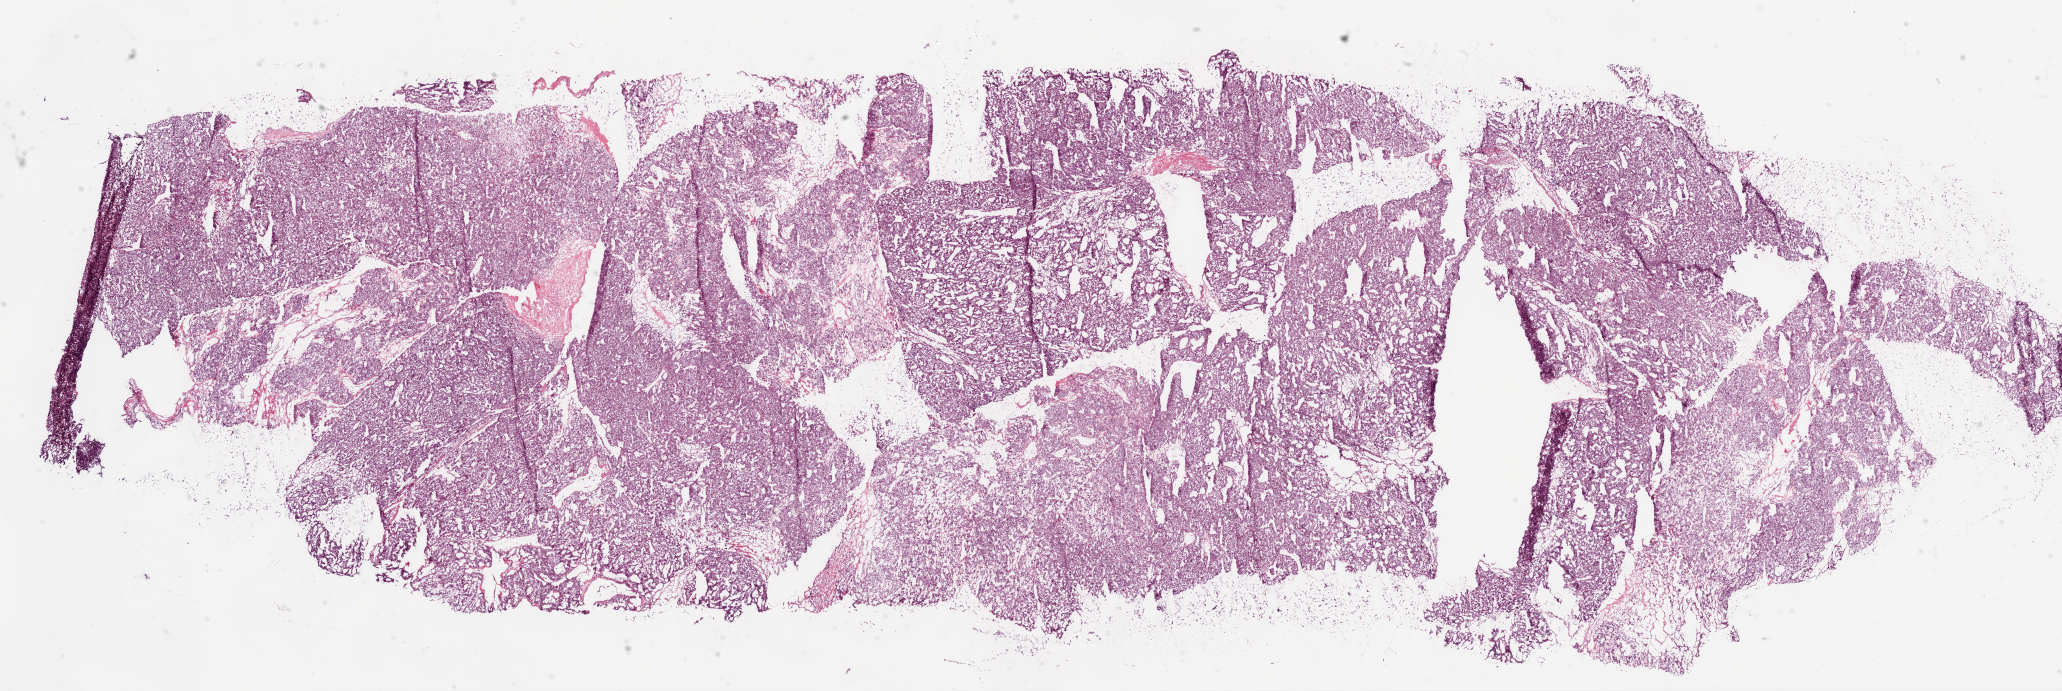
Whole-slide histology image, Hematoxylin and eosin (H&E) stained, low-resolution overview of the scanned area, about 33.1 x 11.1 mm (slide scanned at 20x). Frozen section from the bottom of the tissue portion. Primary tumour sample from the kidney. Male patient; age at initial diagnosis 57 years. Histologic grade: G3 (poorly differentiated). Slide review estimates, as recorded: tumour cells 90%, tumour nuclei 85%, normal cells 0%, stromal cells 10%, necrosis 0%.
Histologic diagnosis: Clear cell adenocarcinoma, NOS. Laterality: left. AJCC pathologic stage: II.